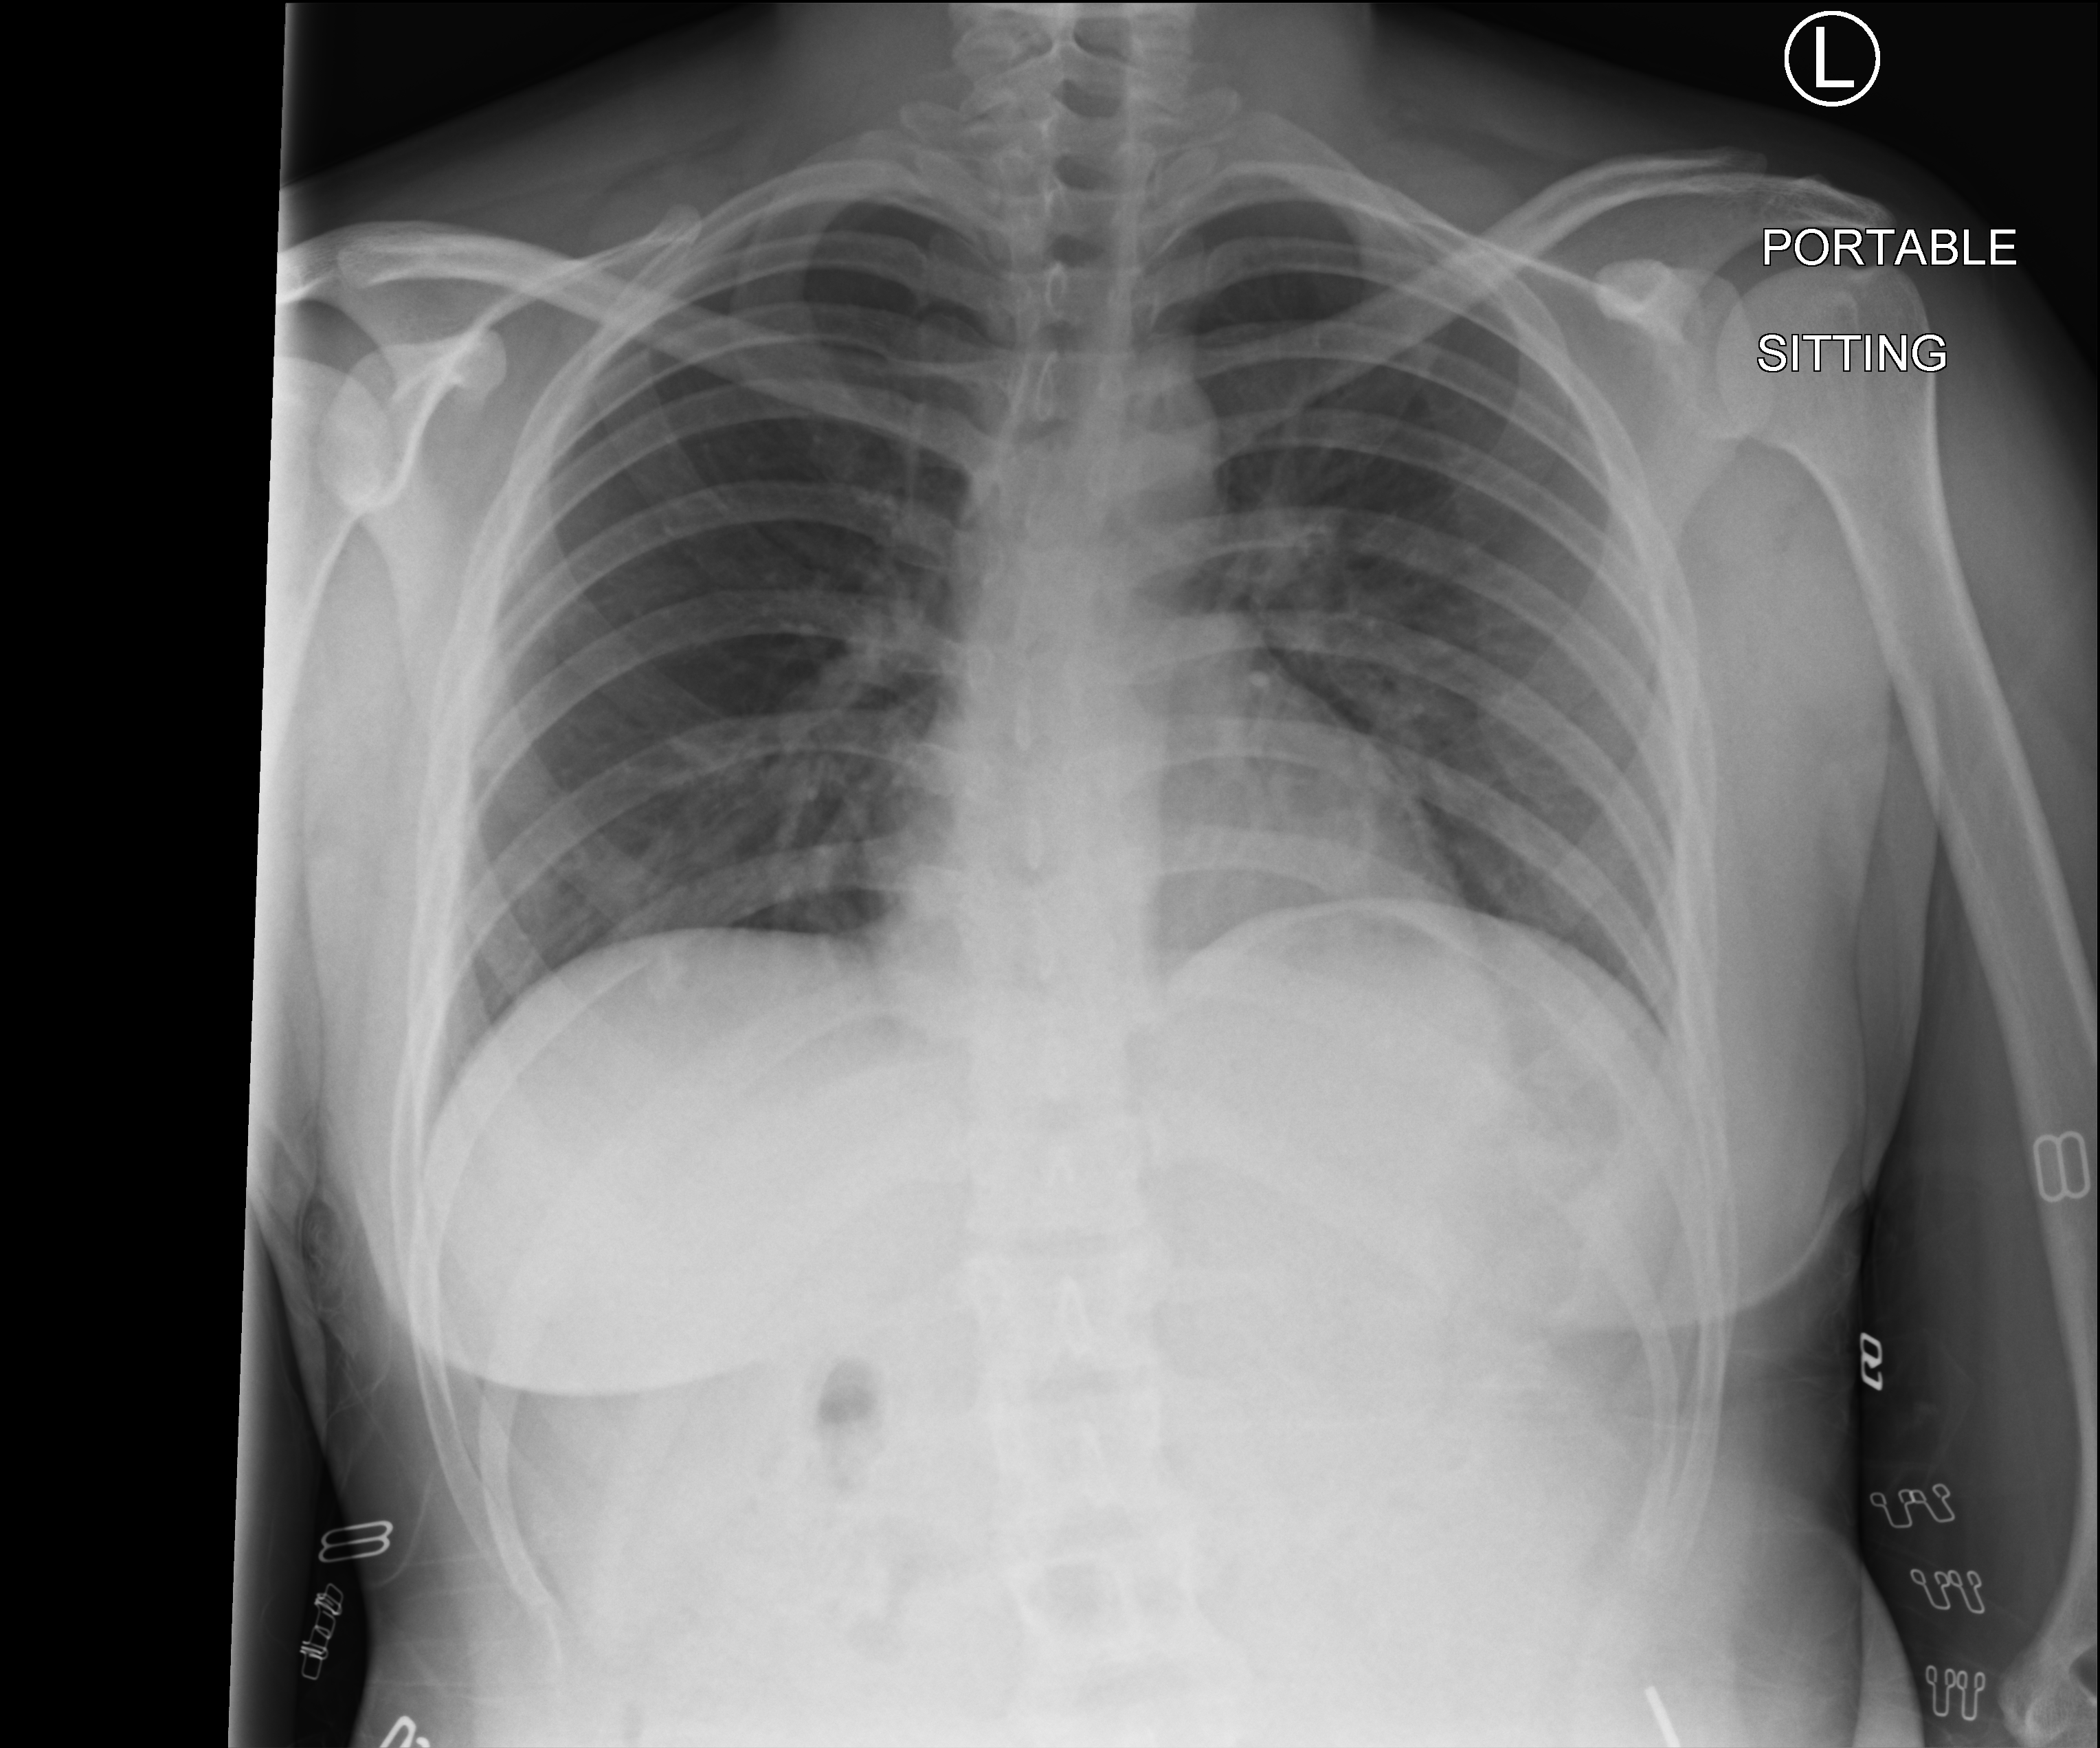
Bedside chest radiograph (computed radiography), anteroposterior (AP) projection. Female patient hospitalised with COVID-19, age 18–59 years.
Hospital-stay facts (about this admission, not read from this image; timing relative to this image not recorded):
- mechanically ventilated during this hospital stay: no
- admitted to intensive care during this hospital stay: no
- COPD (admission record): no